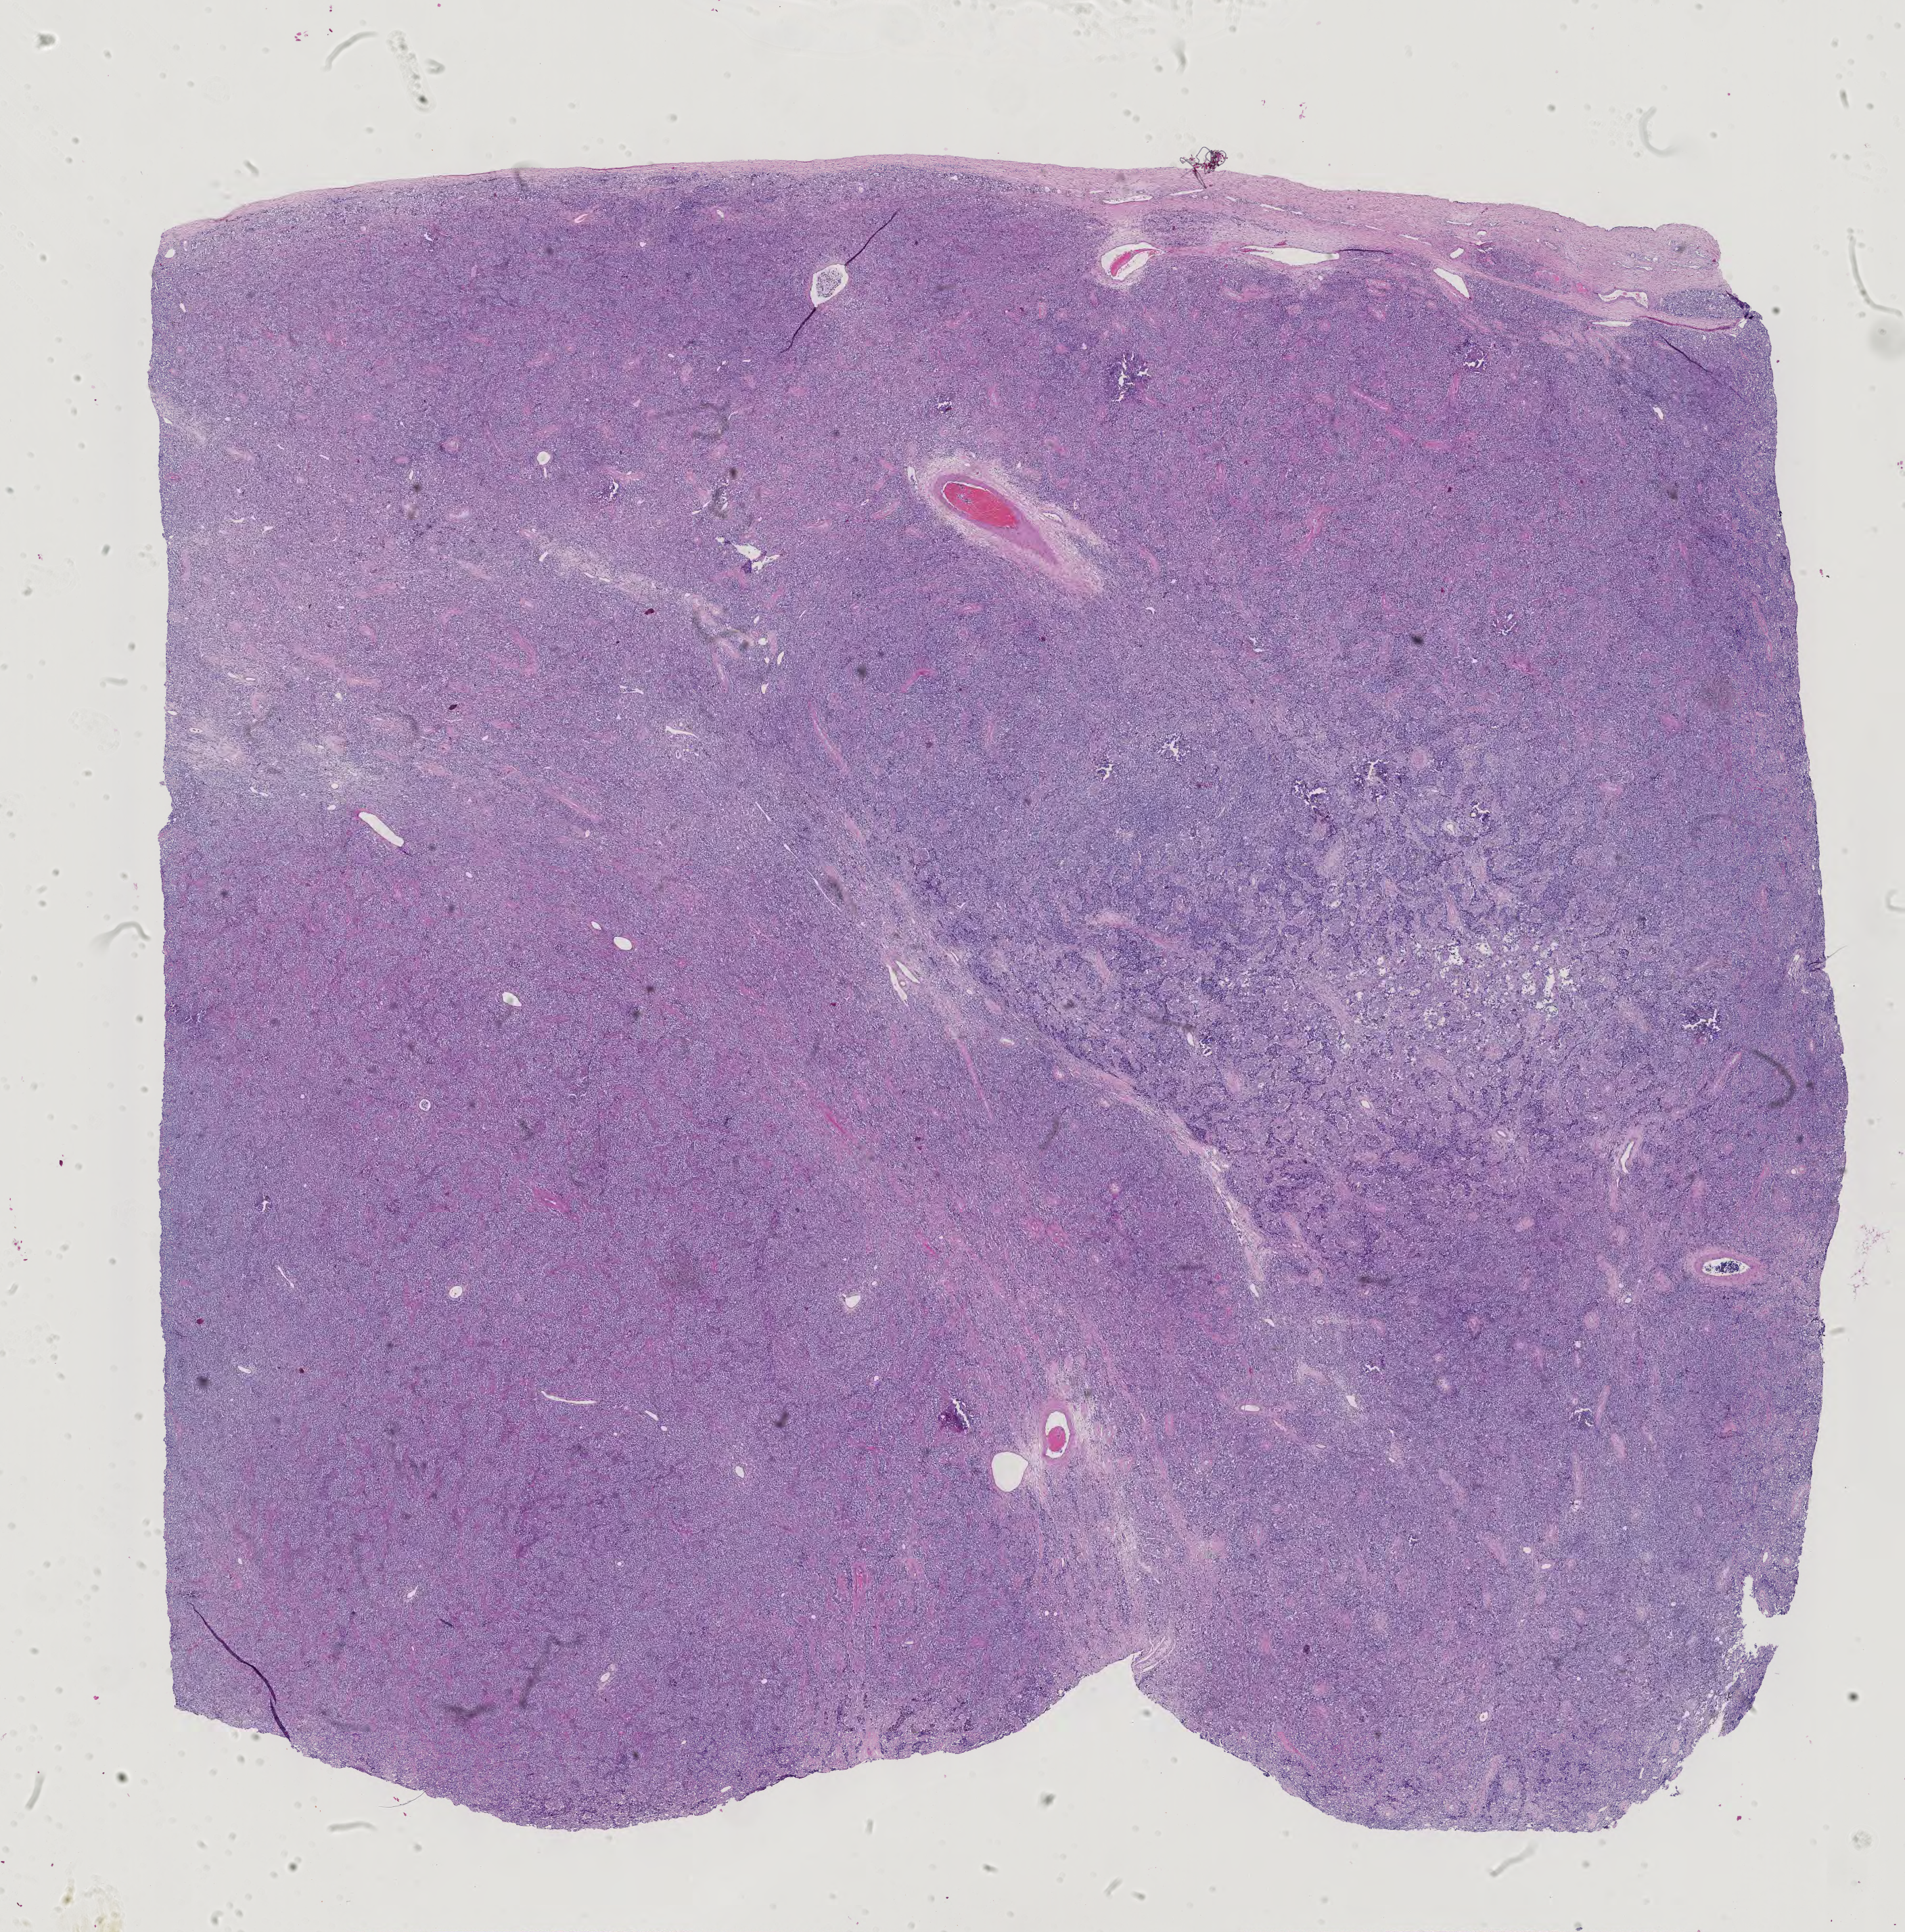
Whole-slide histology image, H&E-stained, shown as a low-resolution overview of the whole scanned area (about 20.5 x 20.8 mm), FFPE section, primary tumour sample from the testis. Patient: male, age at initial diagnosis 31 years.
Diagnosis: Seminoma, NOS. AJCC pathologic stage: IS (7th edition).